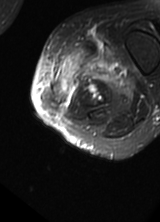
MRI of an extremity soft-tissue mass, one axial slice. Slice 11 of 69 in the series (ordered by position). T2-weighted fat-saturated. MR volume resampled by the dataset authors to the PET/CT grid (not the native acquisition matrix). 160 × 222 image matrix, field of view 156 × 217 mm. Female patient. From the clinical record (not read from this slice): histological type: pleomorphic leiomyosarcoma; grade: high; site of the primary tumour: left thigh.
Annotated regions visible in this slice (expert contour drawn on MRI and transferred to this co-registered scan by the dataset authors):
- gross tumour volume including surrounding oedema: bounding box [x1, y1, x2, y2] px = [50, 38, 133, 110]